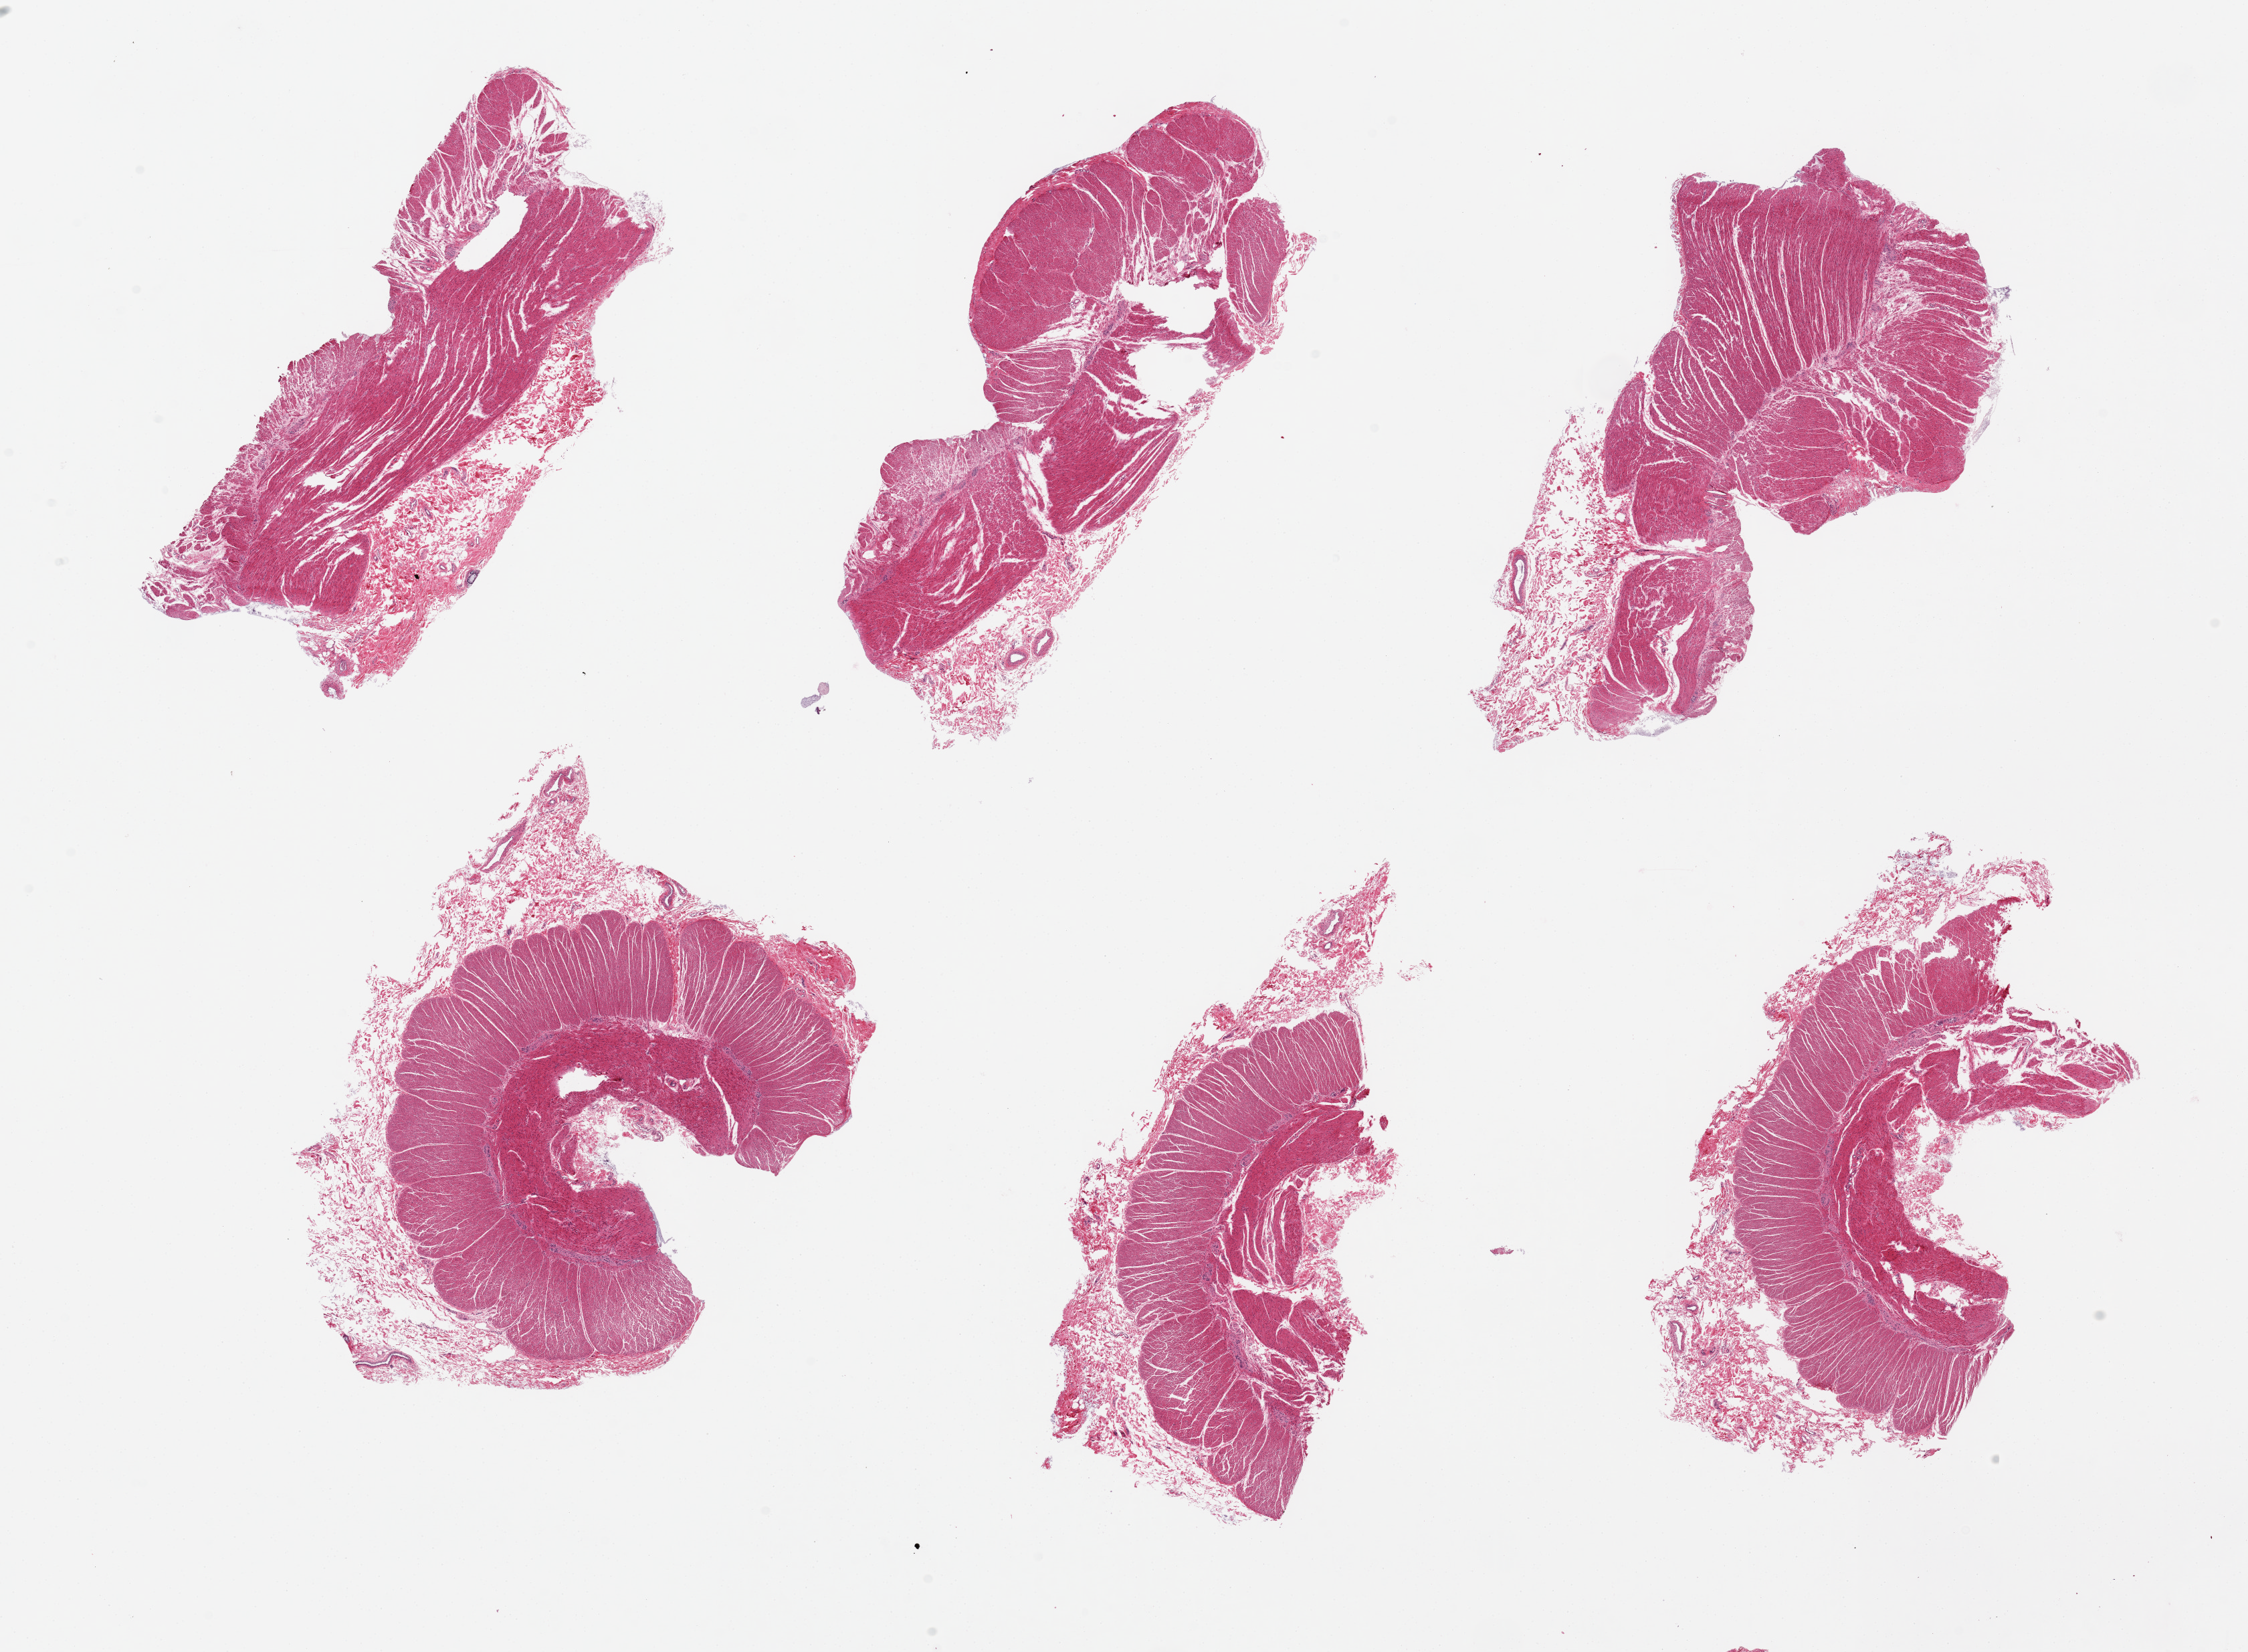
Hematoxylin and eosin (H&E) whole-slide image, brightfield, shown as a low-resolution overview of the whole scanned area (about 26.6 x 19.5 mm, acquisition: 20x scan). PAXgene-fixed paraffin-embedded (PFPE) section. Target tissue: sigmoid colon. Tissue donor sample. Male donor.
Review note (as recorded): 6 pieces. up to 8x5mm; All muscle (target) with adjacent submucosa. Neural tissue marked.